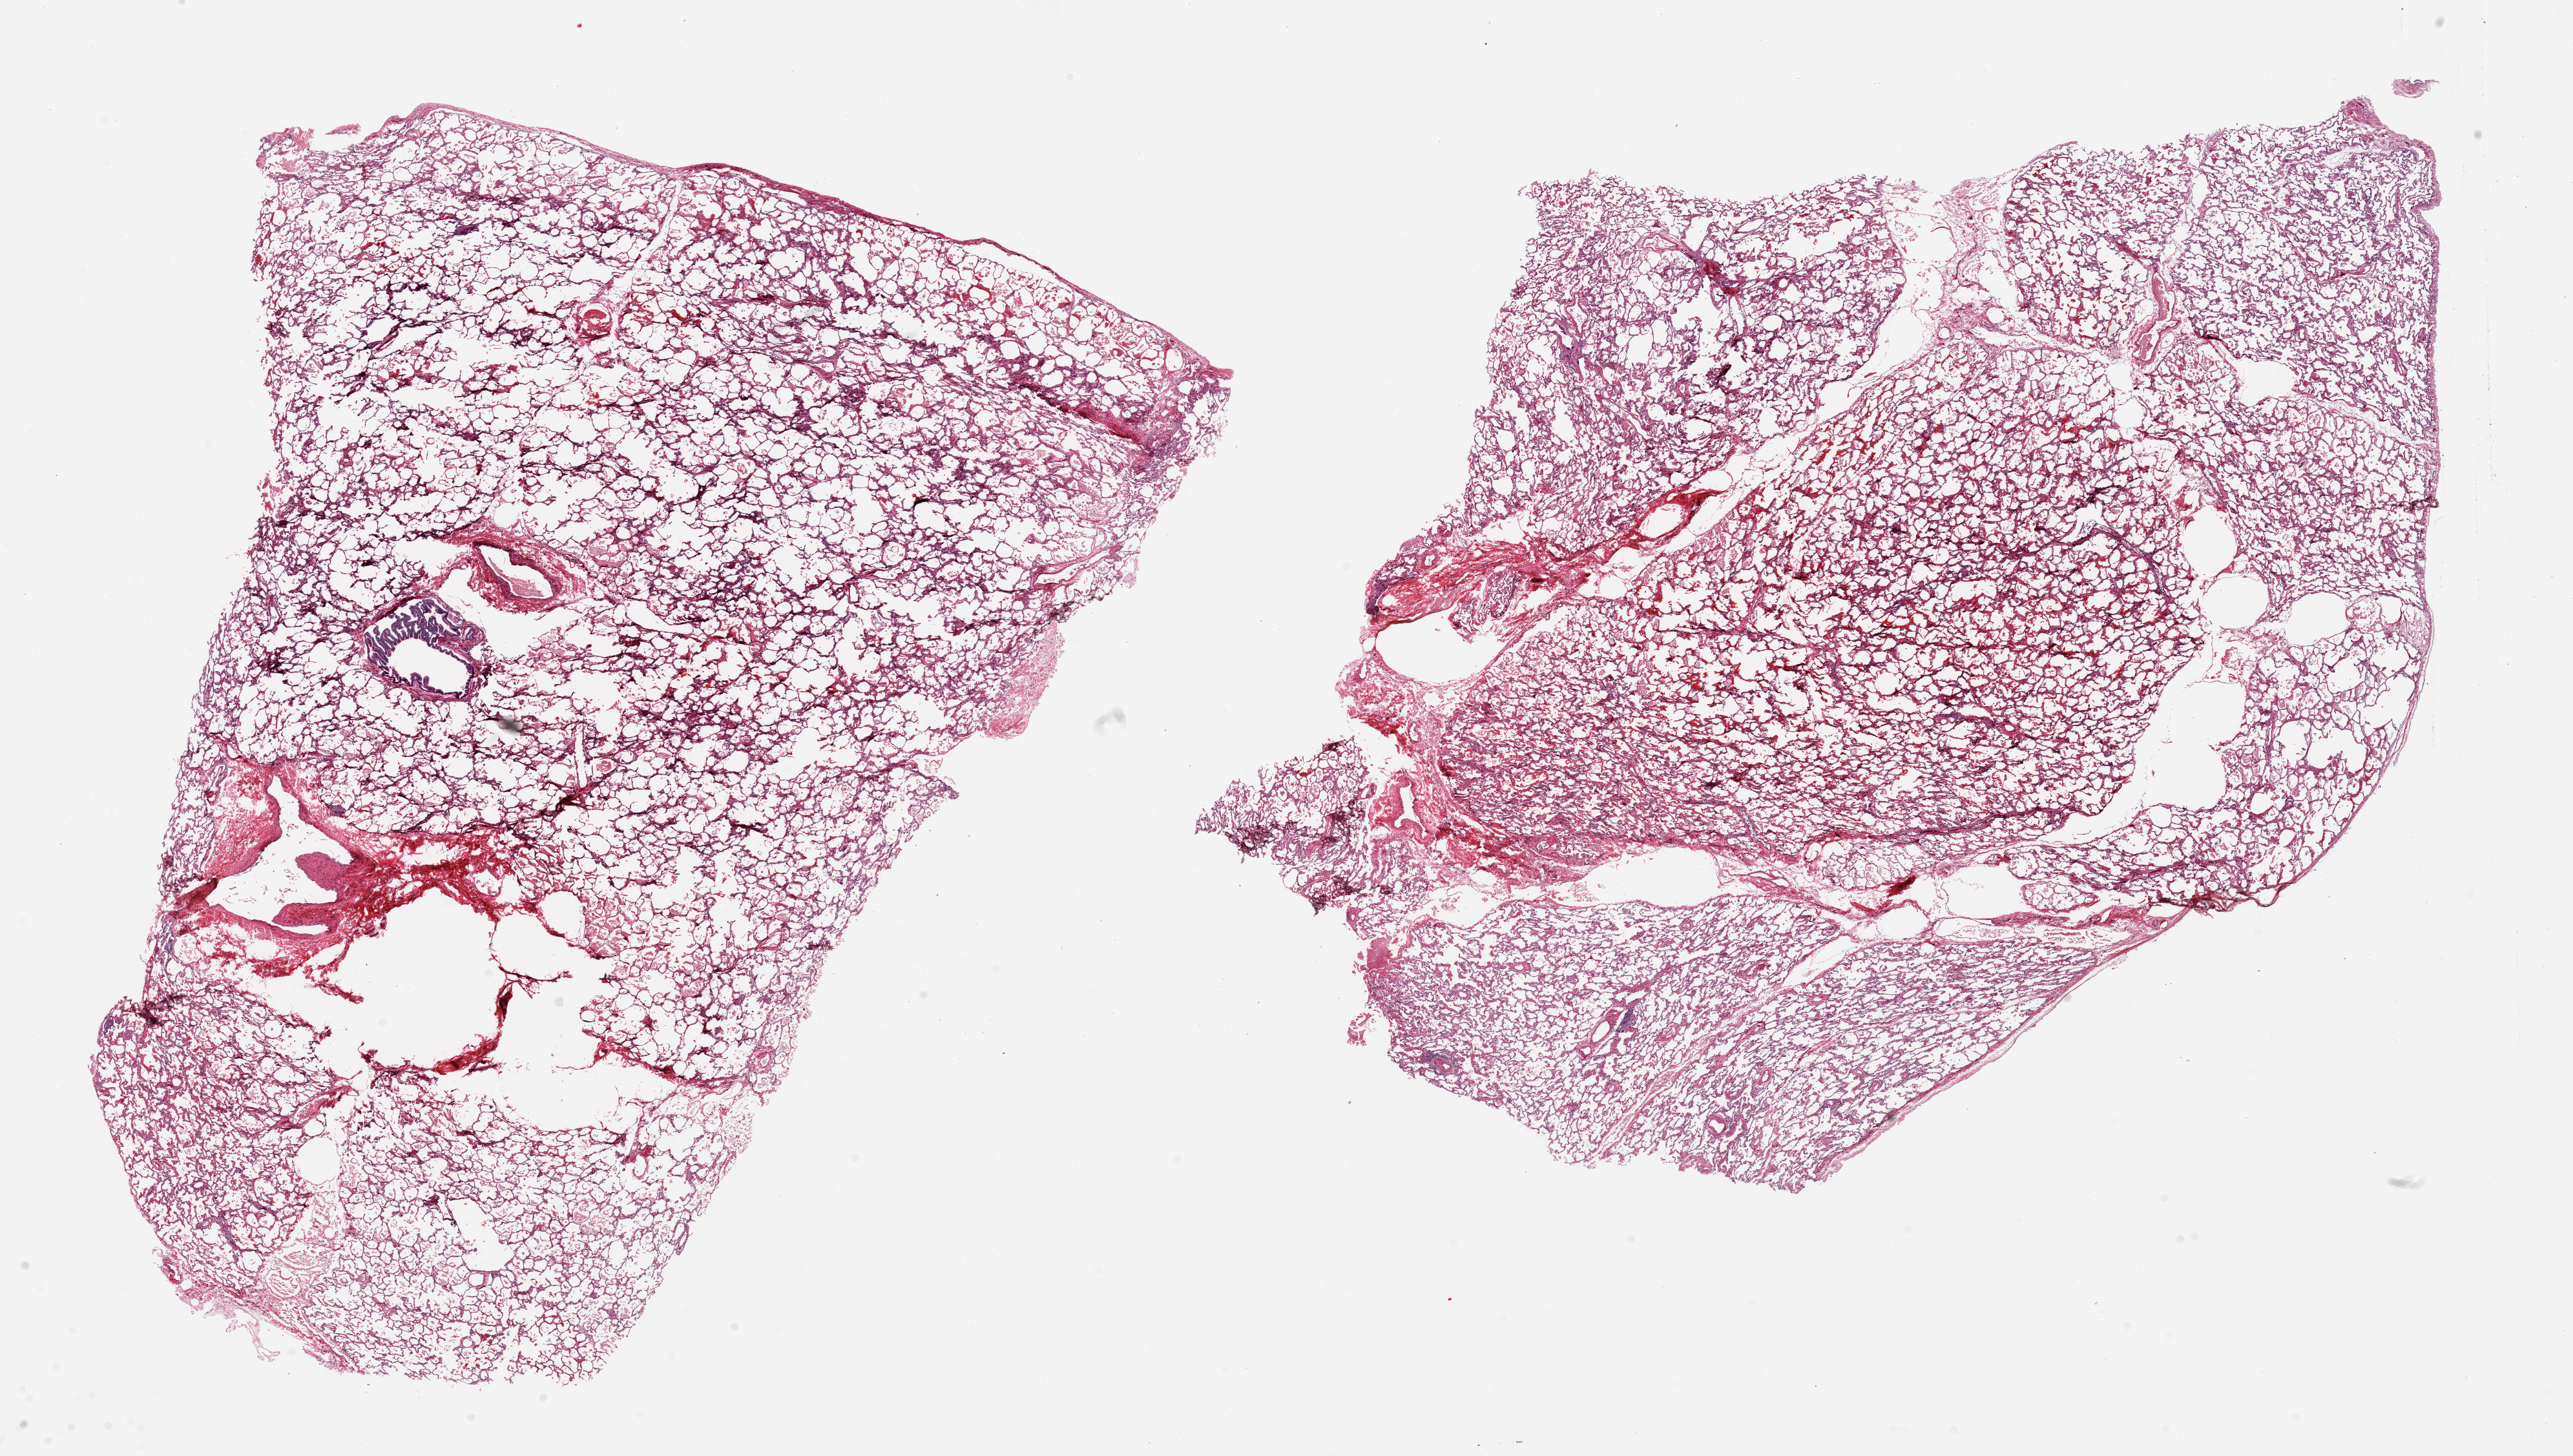
Whole-slide image, hematoxylin and eosin (H&E) stain, a low-resolution overview of the entire scanned area, about 31.5 x 17.8 mm; PAXgene-fixed paraffin-embedded (PFPE) section; sampled site (target tissue): lung; donor tissue sample. Female donor.
Review note (as recorded): 2 pieces; over-sized and poorly fixed, includes pleura (not target).